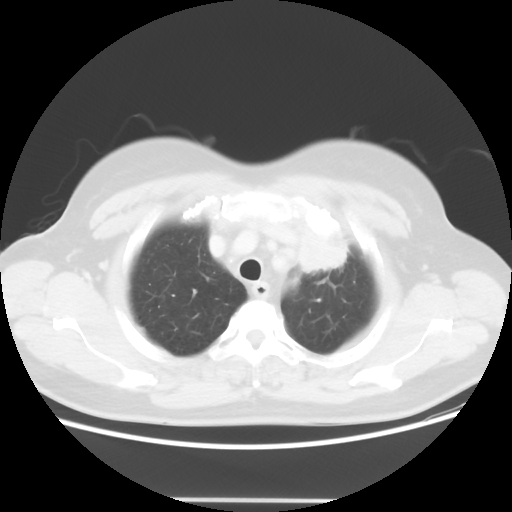
Chest CT, one axial slice. Slice 45 of 52 in the series (ordered by position). Lung window (W 1500 / L -600 HU). 5 mm slice thickness. 512 × 512 image matrix. Female patient, age 52 years. Case-level facts recorded for this patient, not image findings: clinical TNM (as recorded): T2 N3 M0.
Outlined on this slice (bounding box drawn by a radiologist):
- lung tumour (recorded histology: adenocarcinoma): bounding box <294,216,354,275> (left, top, right, bottom; pixels)